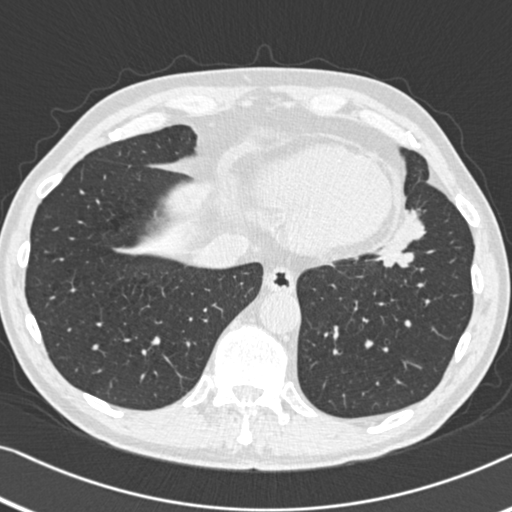
Low-dose screening chest CT, one axial slice; slice 126 of 383 in the series (ordered by position); reconstruction kernel B30f; lung window (W 1500 / L -600 HU); 1 mm slice thickness; 512 × 512 image matrix, field of view 332 × 332 mm.
Outlined on this slice (expert manual segmentation):
- lesion 1 (tumor, upper lobe of left lung): bounding box <378,210,425,268> (left, top, right, bottom; pixels)